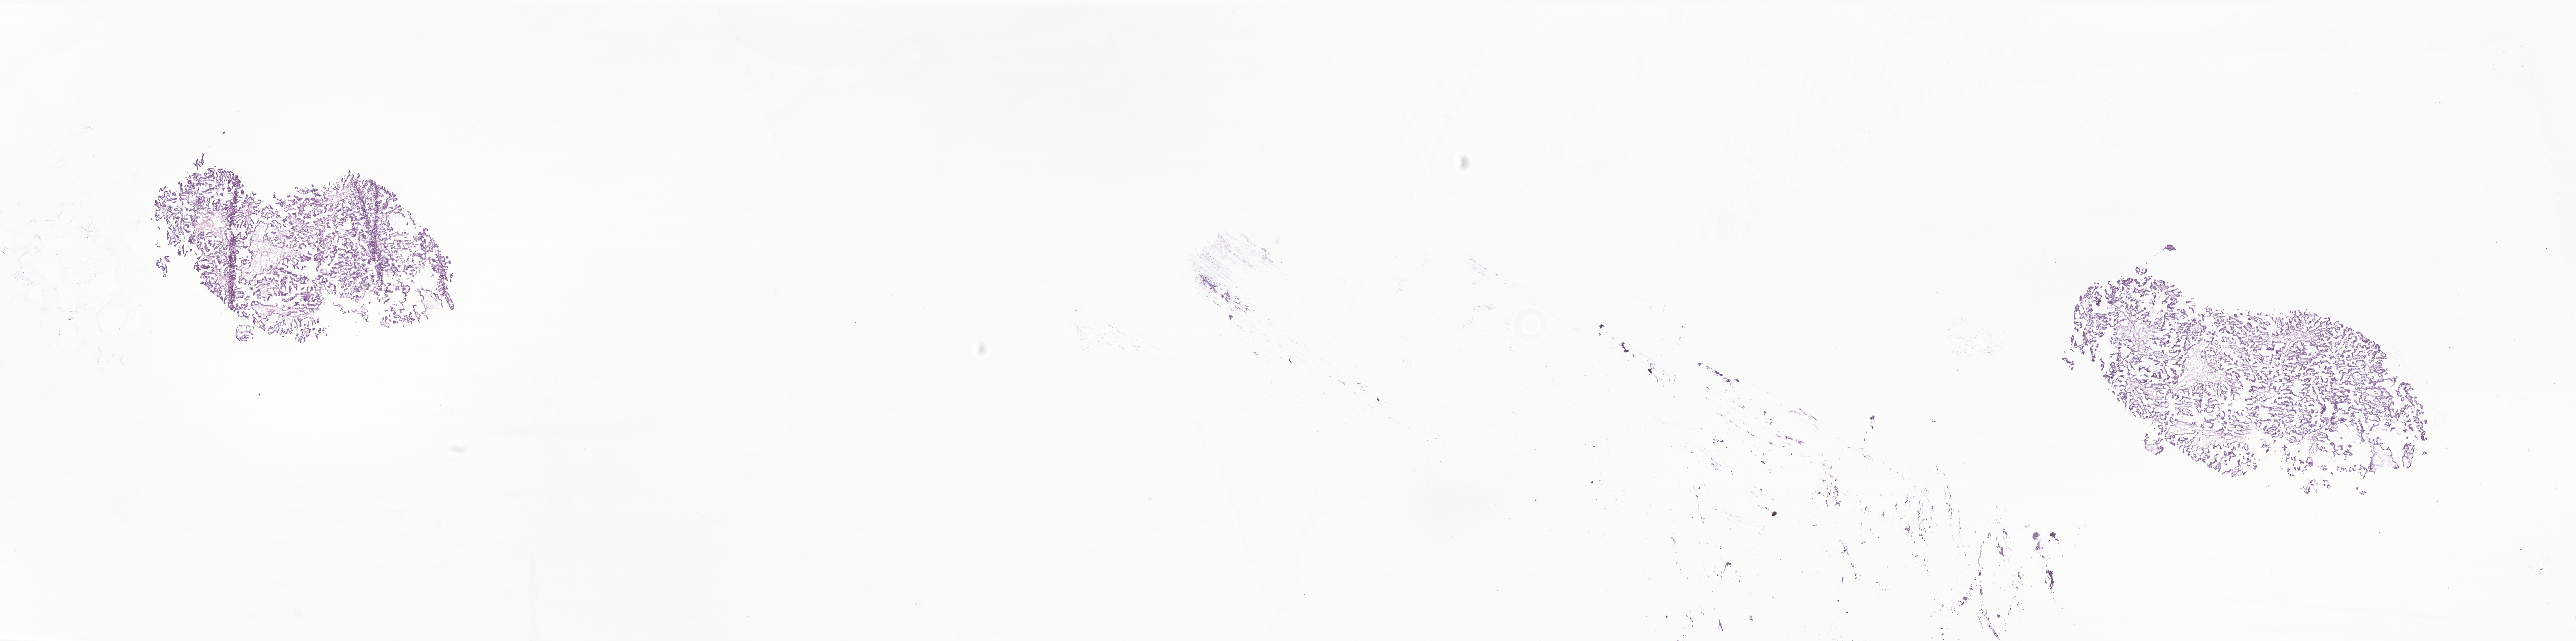
Whole-slide image, haematoxylin and eosin stain of tumor tissue from the cerebral ventricle — a low-resolution overview of the entire scanned area, about 31.5 x 7.8 mm; frozen section. Male patient, age 220 days.
Diagnosis: Choroid plexus papilloma, NOS.